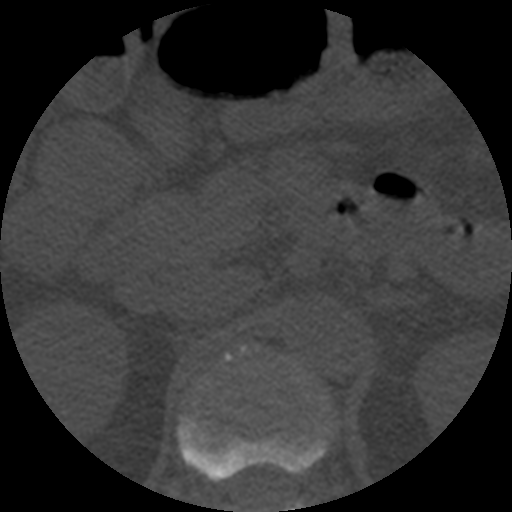
CT including the spine, one axial slice; slice 202 of 508 in the series (ordered by position); bone window (W 1800 / L 400 HU); 1.25 mm slice thickness; 512 × 512 image matrix. Patient age 57 years. Case-level facts recorded for this patient, not image findings: primary cancer: prostate.
Annotated regions visible in this slice (semi-automatically segmented with operator editing):
- L1 vertebra: bounding box <289,502,304,512> (left, top, right, bottom; pixels)
- T12 vertebra: <178,414,329,482>